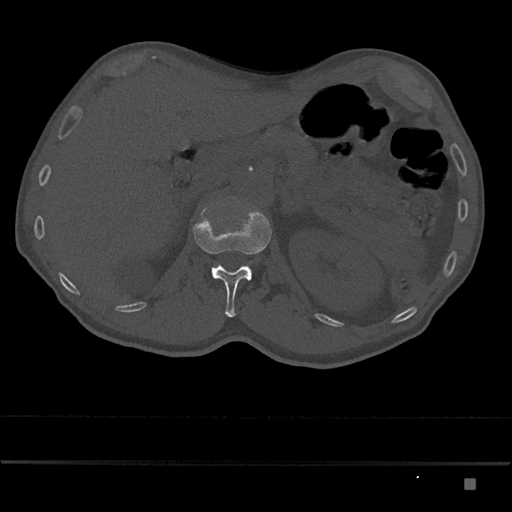
CT including the spine, one axial slice. Position 535 of 797 along the scan axis. Bone window (W 1800 / L 400 HU). 0.5 mm slice thickness. 512 × 512 image matrix. Patient: male, 72 years. Case-level facts recorded for this patient, not image findings: primary cancer: prostate.
Annotated regions visible in this slice (semi-automatic segmentation, software-assisted and operator-edited):
- L1 vertebra: bounding box (x1, y1, x2, y2) in pixels: (193, 209, 272, 317)